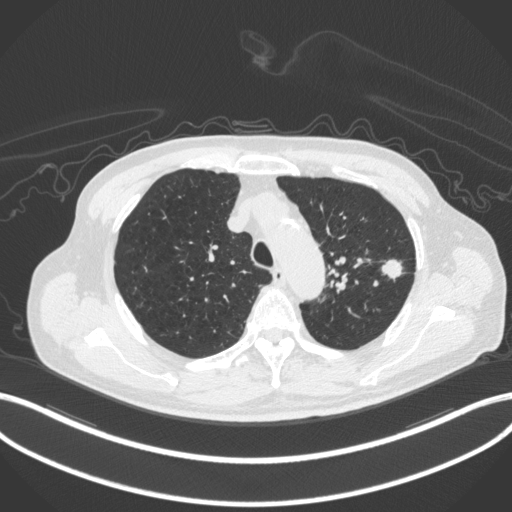
Chest CT, one axial slice. Position 340 of 420 along the scan axis. Reconstruction kernel B31f. 120 kVp. Lung window (W 1500 / L -600 HU). 512 × 512 image matrix, field of view 400 × 400 mm. Patient: male, 77 years. From the clinical record (not read from this slice): clinical TNM (as recorded): T3 N1 M0.
Annotated regions visible in this slice (rectangle marked by the reading radiologist):
- lung tumour (recorded histology: adenocarcinoma): bounding box <379,257,406,279> (left, top, right, bottom; pixels)